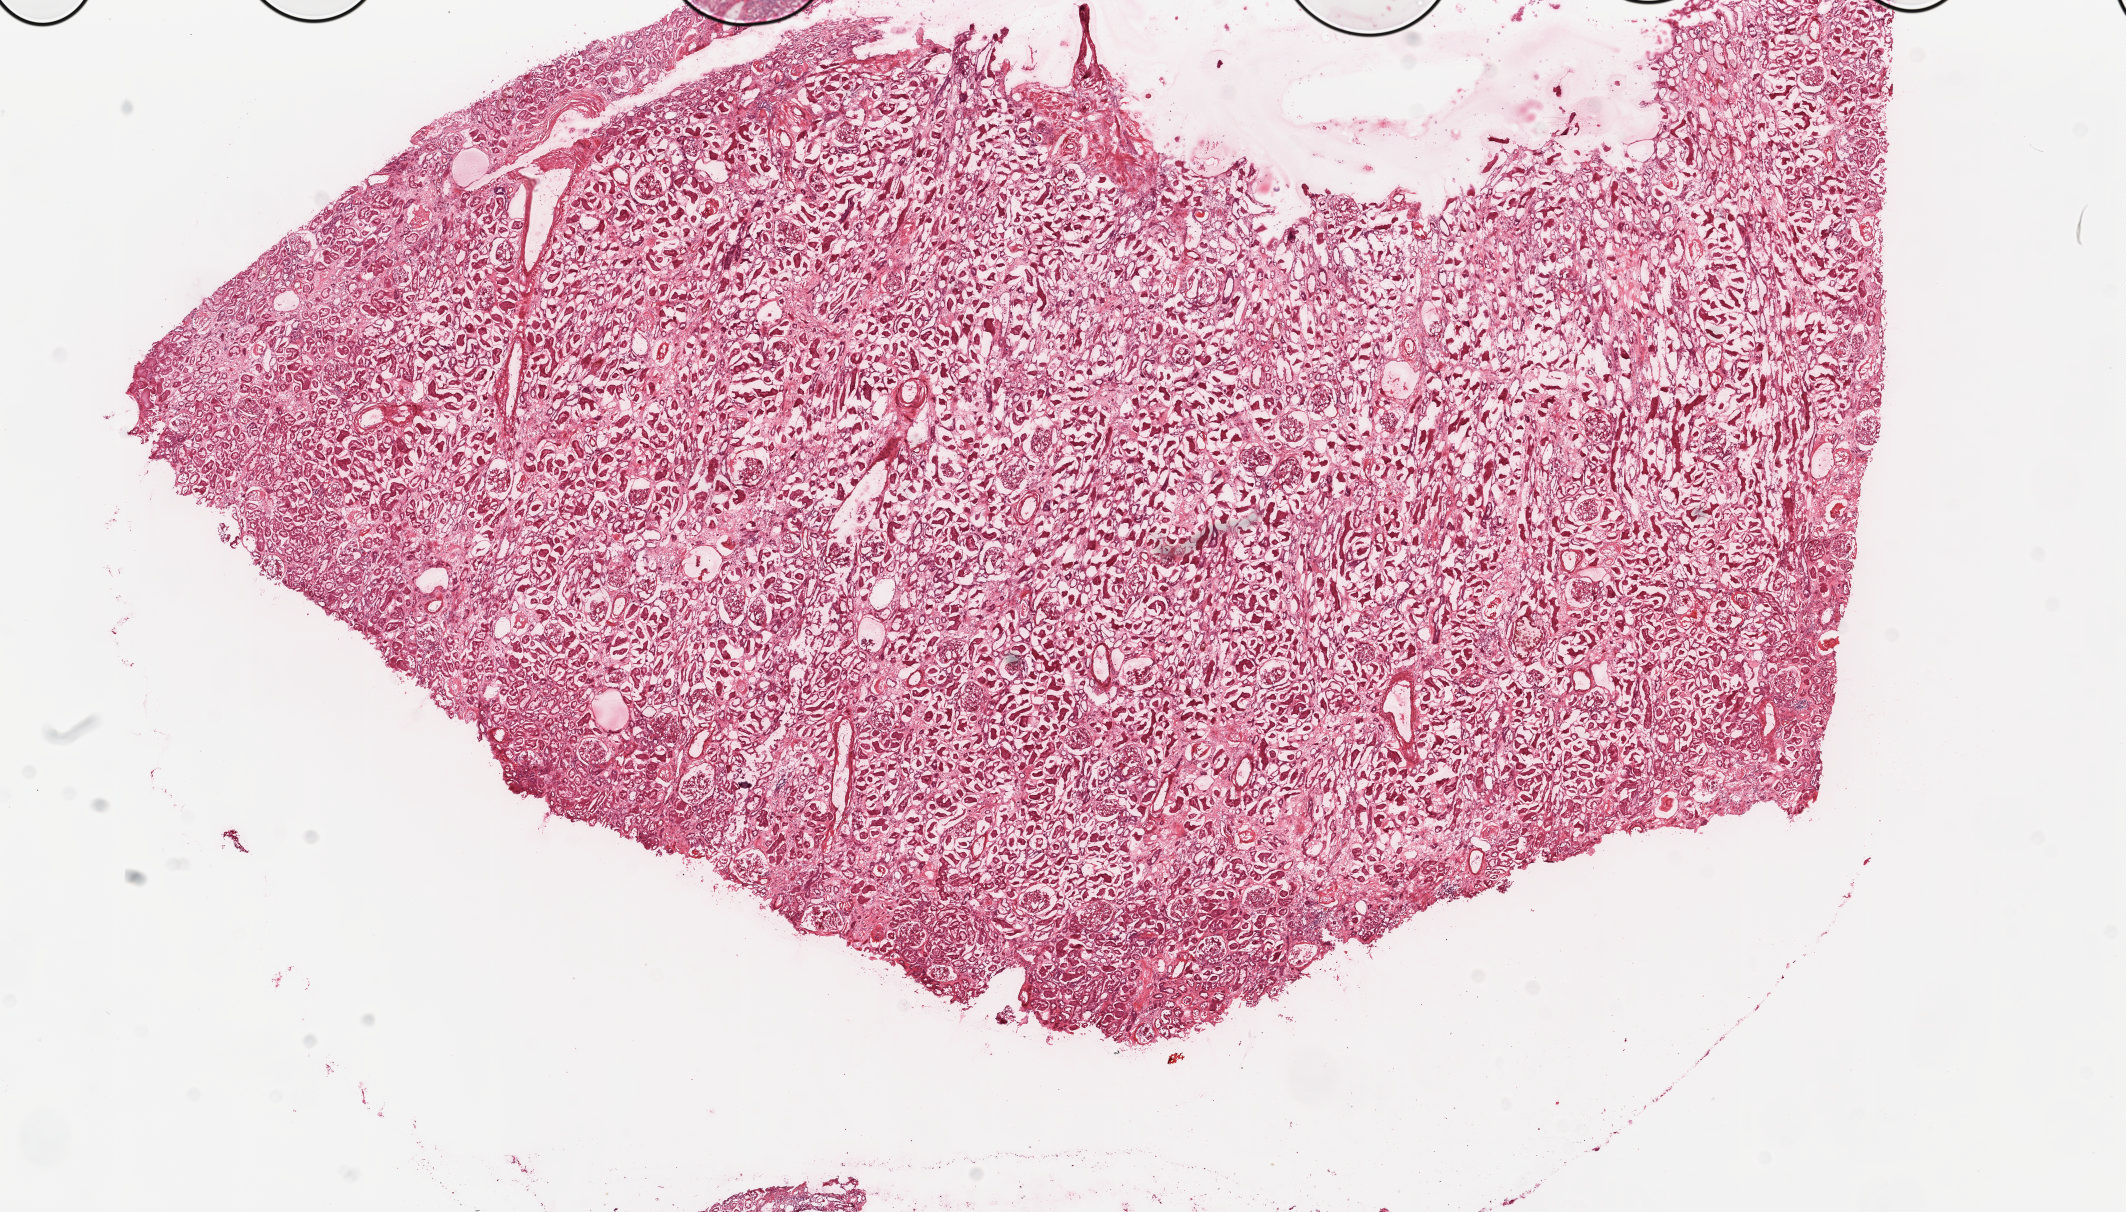
Digitized H&E tissue section (whole slide) — whole scanned area (about 16.9 x 9.6 mm) shown as a low-resolution overview; frozen section from the top of the tissue portion; sample: solid tissue normal (non-tumour tissue), kidney. Male patient; age at initial diagnosis 81 years.
This section: solid tissue normal sample (biorepository sample class). Patient diagnosis: Clear cell adenocarcinoma, NOS.